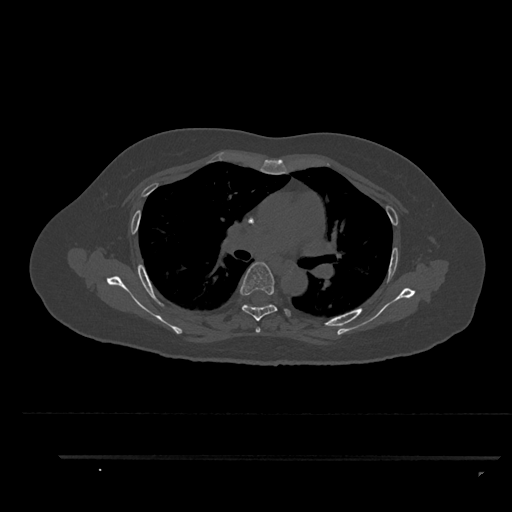
CT including the spine, one axial slice; position 599 of 797 along the scan axis; bone window (W 1800 / L 400 HU); 512 × 512 image matrix. Female patient, age 44 years. Case-level facts recorded for this patient, not image findings: primary cancer: renal; vertebrae with lytic lesions (as recorded): L1.
Outlined on this slice (semi-automatically segmented with operator editing):
- T4 vertebra: box from (x=256, y=327) to (x=261, y=333) px
- T5 vertebra: (x=240, y=262)–(x=291, y=321)
- T6 vertebra: (x=244, y=304)–(x=270, y=307)